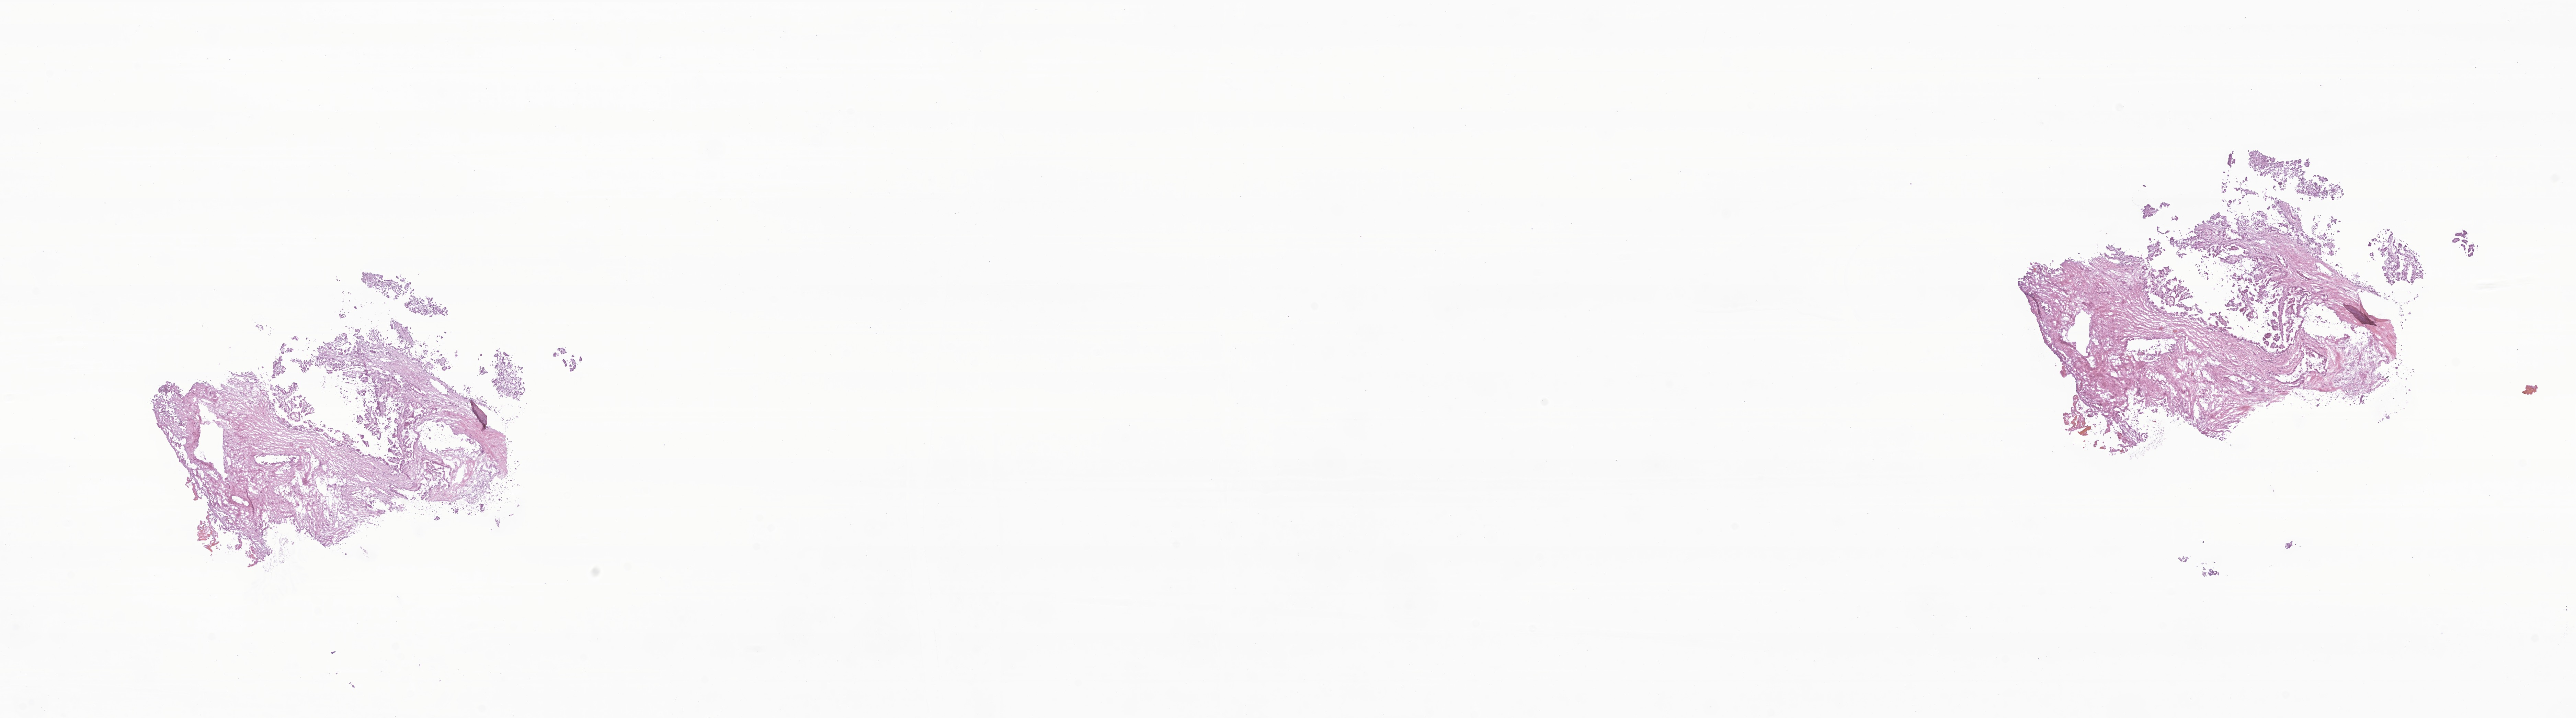
Digitized hematoxylin and eosin (H&E)-stained section of tumor tissue from the brain — a low-resolution overview of the entire scanned area, about 31.6 x 8.8 mm; cryosection (OCT / tissue freezing medium). Patient: male, age 611 days.
Diagnosis (ICD-O-3 morphology term): Choroid plexus papilloma, NOS.